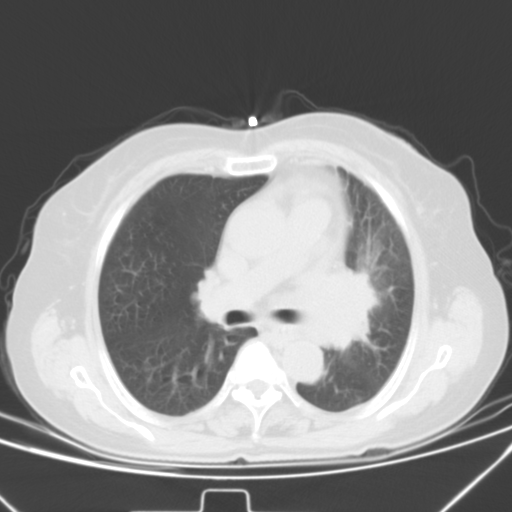
Chest CT, one axial slice. Lung window (W 1500 / L -600 HU). 512 × 512 image matrix, field of view 331 × 331 mm. Patient: female, 59 years. From the clinical record (not read from this slice): clinical TNM (as recorded): T3 N1 M0.
Structures marked on this image (bounding box drawn by a radiologist):
- lung tumour (recorded histology: small cell carcinoma): bounding box (x1, y1, x2, y2) in pixels: (315, 264, 381, 350)